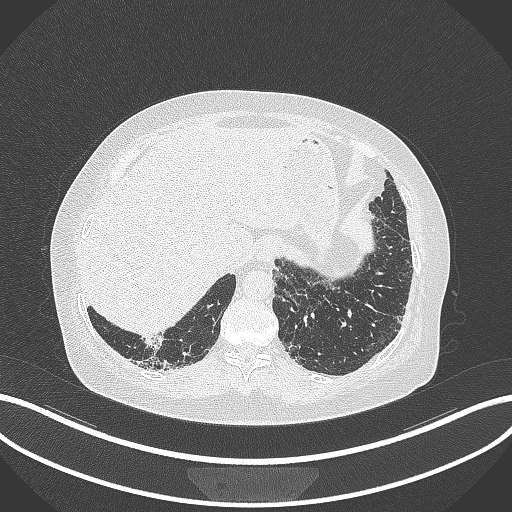
Chest CT, one axial slice. Slice 11 of 296 in the series (ordered by position). Reconstruction kernel B70f. Lung window (W 1500 / L -600 HU). 1 mm slice thickness. 512 × 512 image matrix, field of view 400 × 400 mm. Female patient, age 65 years. Case-level facts recorded for this patient, not image findings: clinical TNM (as recorded): T2b N1 M0; histopathological grade: G1.
Structures marked on this image (bounding box drawn by a radiologist):
- lung tumour (recorded histology: adenocarcinoma): bounding box <144,333,166,355> (left, top, right, bottom; pixels)